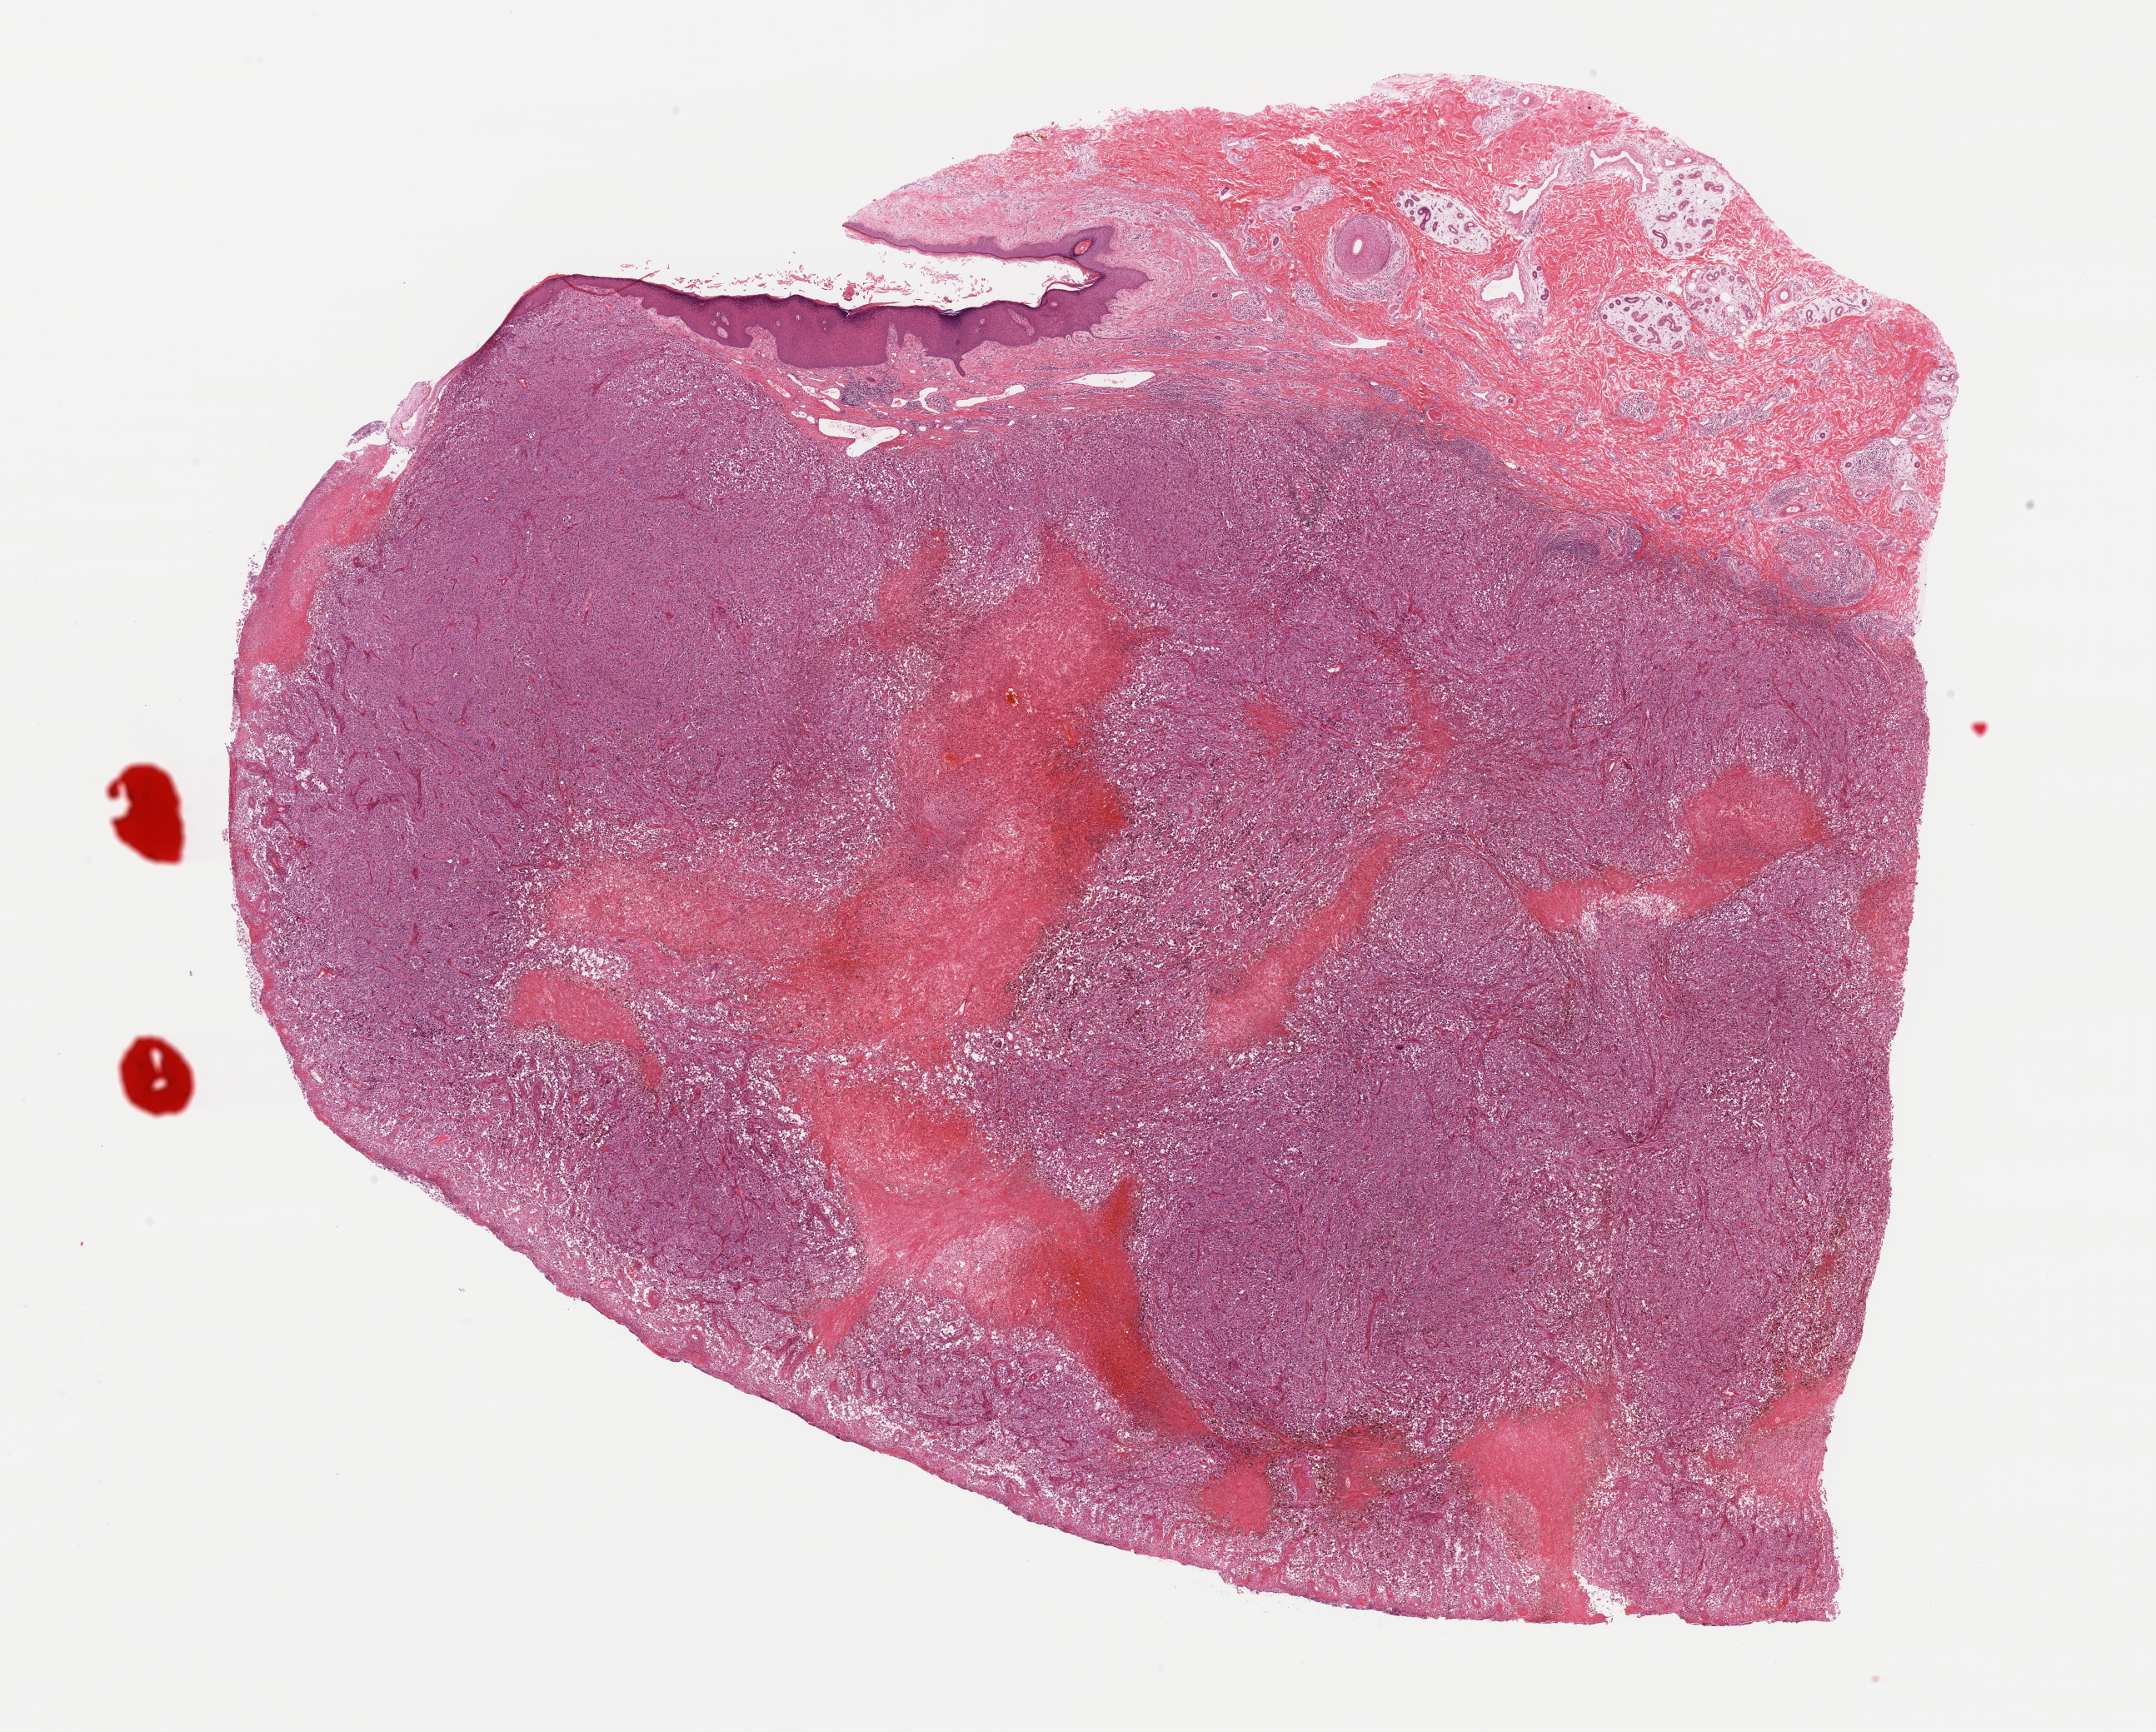
Hematoxylin and eosin (H&E) stained whole-slide image, a low-resolution overview of the entire scanned area, about 20.4 x 16.4 mm (from a 40x scan), FFPE section, sample: primary tumour, skin. Male, age 62 years at initial diagnosis.
* histologic diagnosis: Malignant melanoma, NOS
* AJCC pathologic stage: IIC (7th edition)